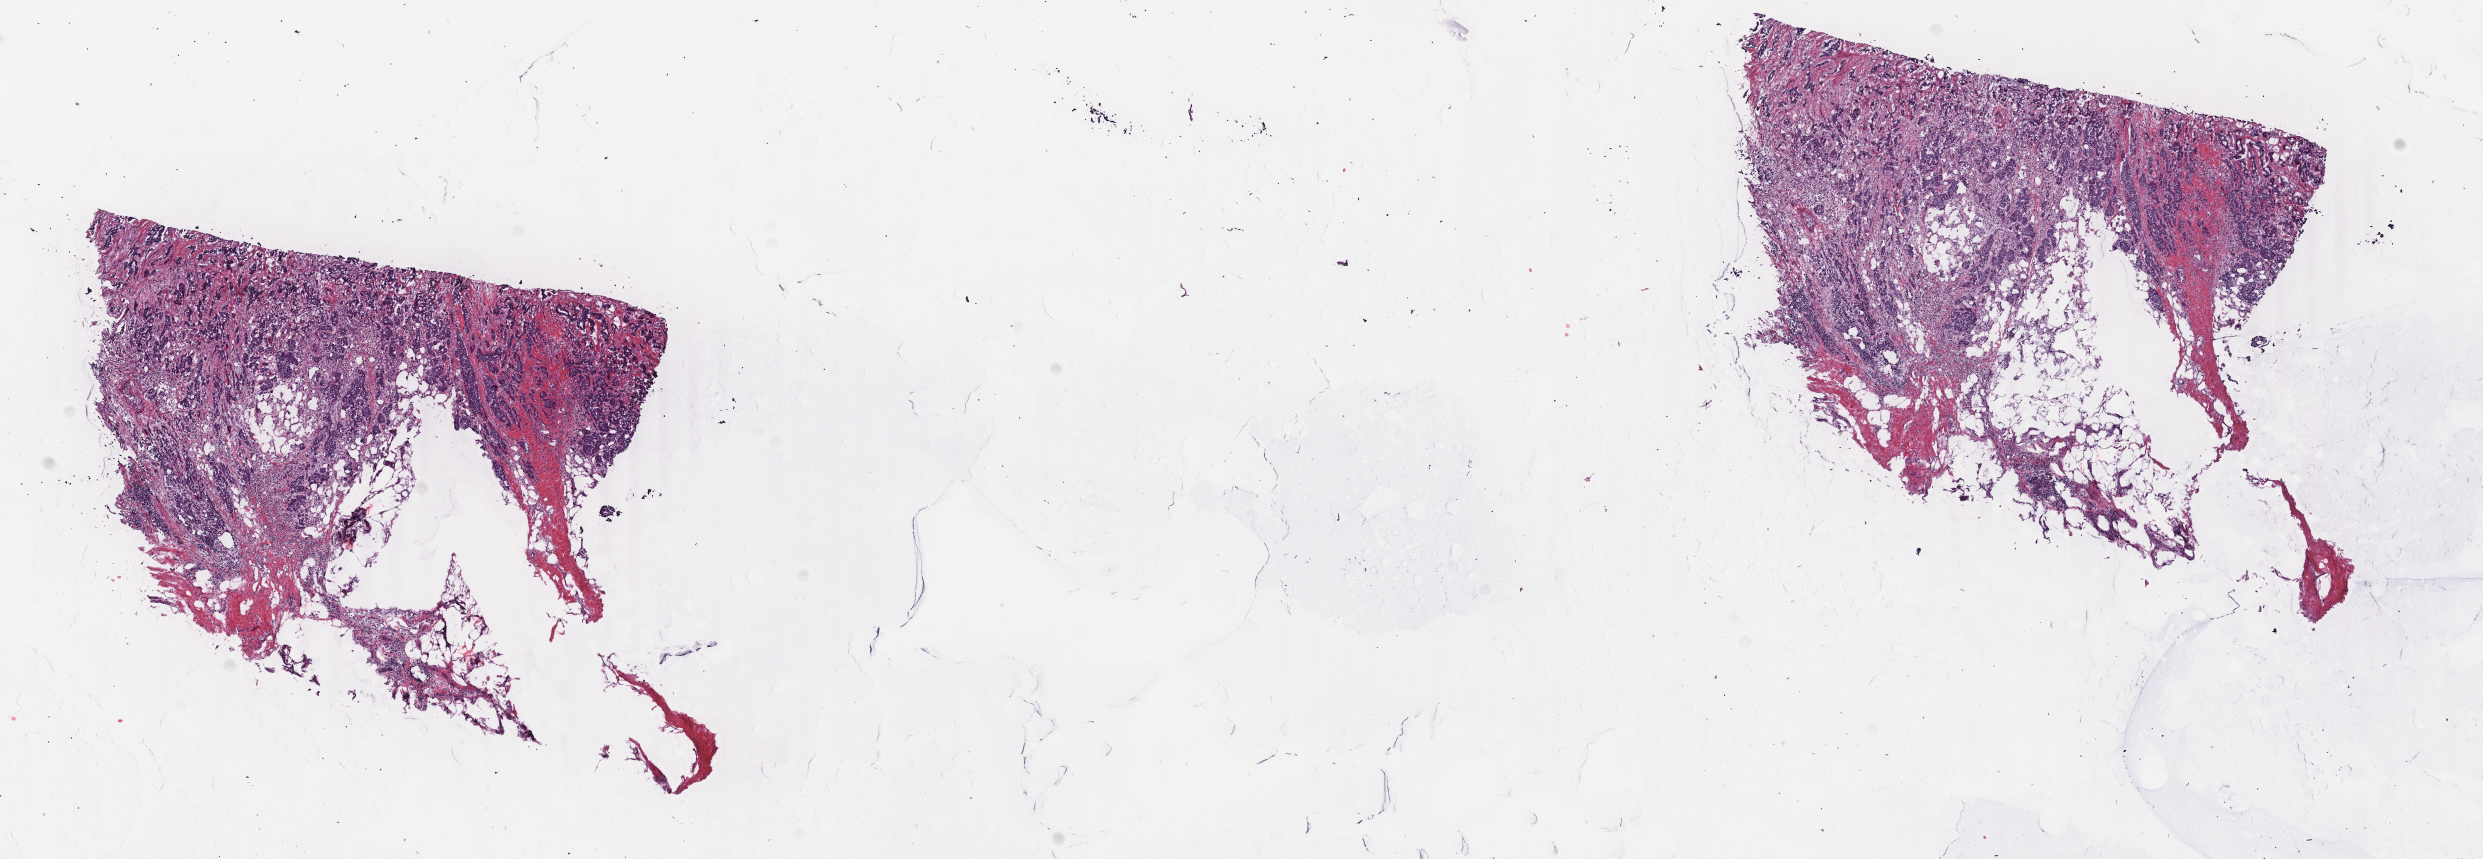
Hematoxylin and eosin (H&E) stained whole-slide image — low-resolution overview of the scanned area, about 19.8 x 6.8 mm (acquisition: 40x scan). Frozen section. Sample: primary tumour, breast. Female patient; age at initial diagnosis 61 years. Pathologist review of this section (percent, as recorded): tumour cells 60%, tumour nuclei 85%, normal cells 0%, stromal cells 40%, necrosis 0%. Inflammatory infiltration, as recorded: lymphocyte infiltration 4%, monocyte infiltration 0%, neutrophil infiltration 0%.
* AJCC pathologic stage: I (6th edition)
* histologic diagnosis: Infiltrating duct carcinoma, NOS
* laterality: right
* TNM: T1 N0 M0